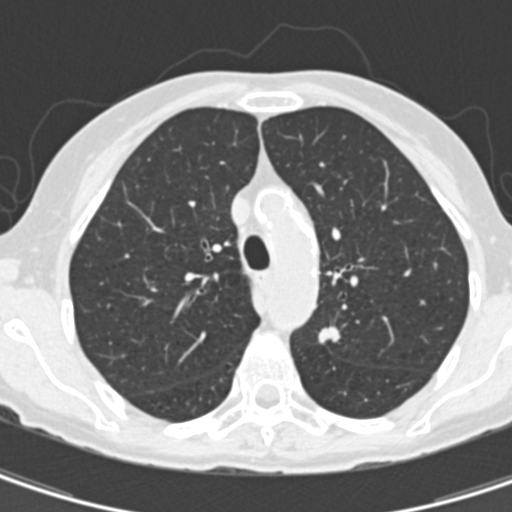
Chest CT (low-dose screening protocol), one axial image. First (baseline) screen. Lung window (W 1500 / L -600 HU). 2 mm slice thickness. Standard (soft-tissue) reconstruction kernel (B30f). Slice 48 of 157 in the series. 512 × 512 image matrix, field of view 260 × 260 mm. Female participant, aged 67 years at enrolment. Current smoker at enrolment.
- Expert reader's lesion annotation, bounding box <312,317,354,366> (left, top, right, bottom; pixels).
- The exam's reader record, not a measurement of the box and not confirmed to be the same lesion: non-calcified nodule or mass ≥4 mm, left upper lobe, 11 × 8 mm, spiculated (stellate) margins, soft tissue attenuation.
- Lung cancer was diagnosed 73 days after this screen: adenocarcinoma, NOS, left upper lobe, poorly differentiated (G3), stage IA (AJCC 6th edition), 13 mm at pathology.